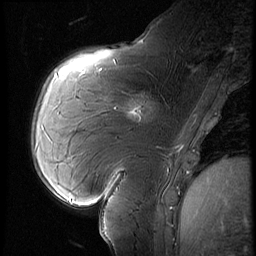
Breast MRI (dynamic contrast-enhanced), one sagittal slice; position 23 of 60 along the scan axis; 3 images stored at this slice position (order not interpretable as contrast timing); 1.5 T; TE 4.2 ms, TR 9 ms; 2.5 mm slice thickness; 256 × 256 image matrix, field of view 180 × 180 mm. Patient: female, 57 years. From the clinical record (not read from this slice): setting: breast cancer imaged before/during neoadjuvant chemotherapy; receptor status: triple-negative.
Outlined on this slice (semi-automatic segmentation, software-assisted and operator-edited):
- analysis volume of interest (the breast-tissue region the enhancement analysis was run in; not a lesion): box from (x=114, y=83) to (x=170, y=131) px
- tumour enhancement mask (voxels above the 140 % enhancement threshold inside the analysis volume of interest): (x=132, y=109)–(x=138, y=113)